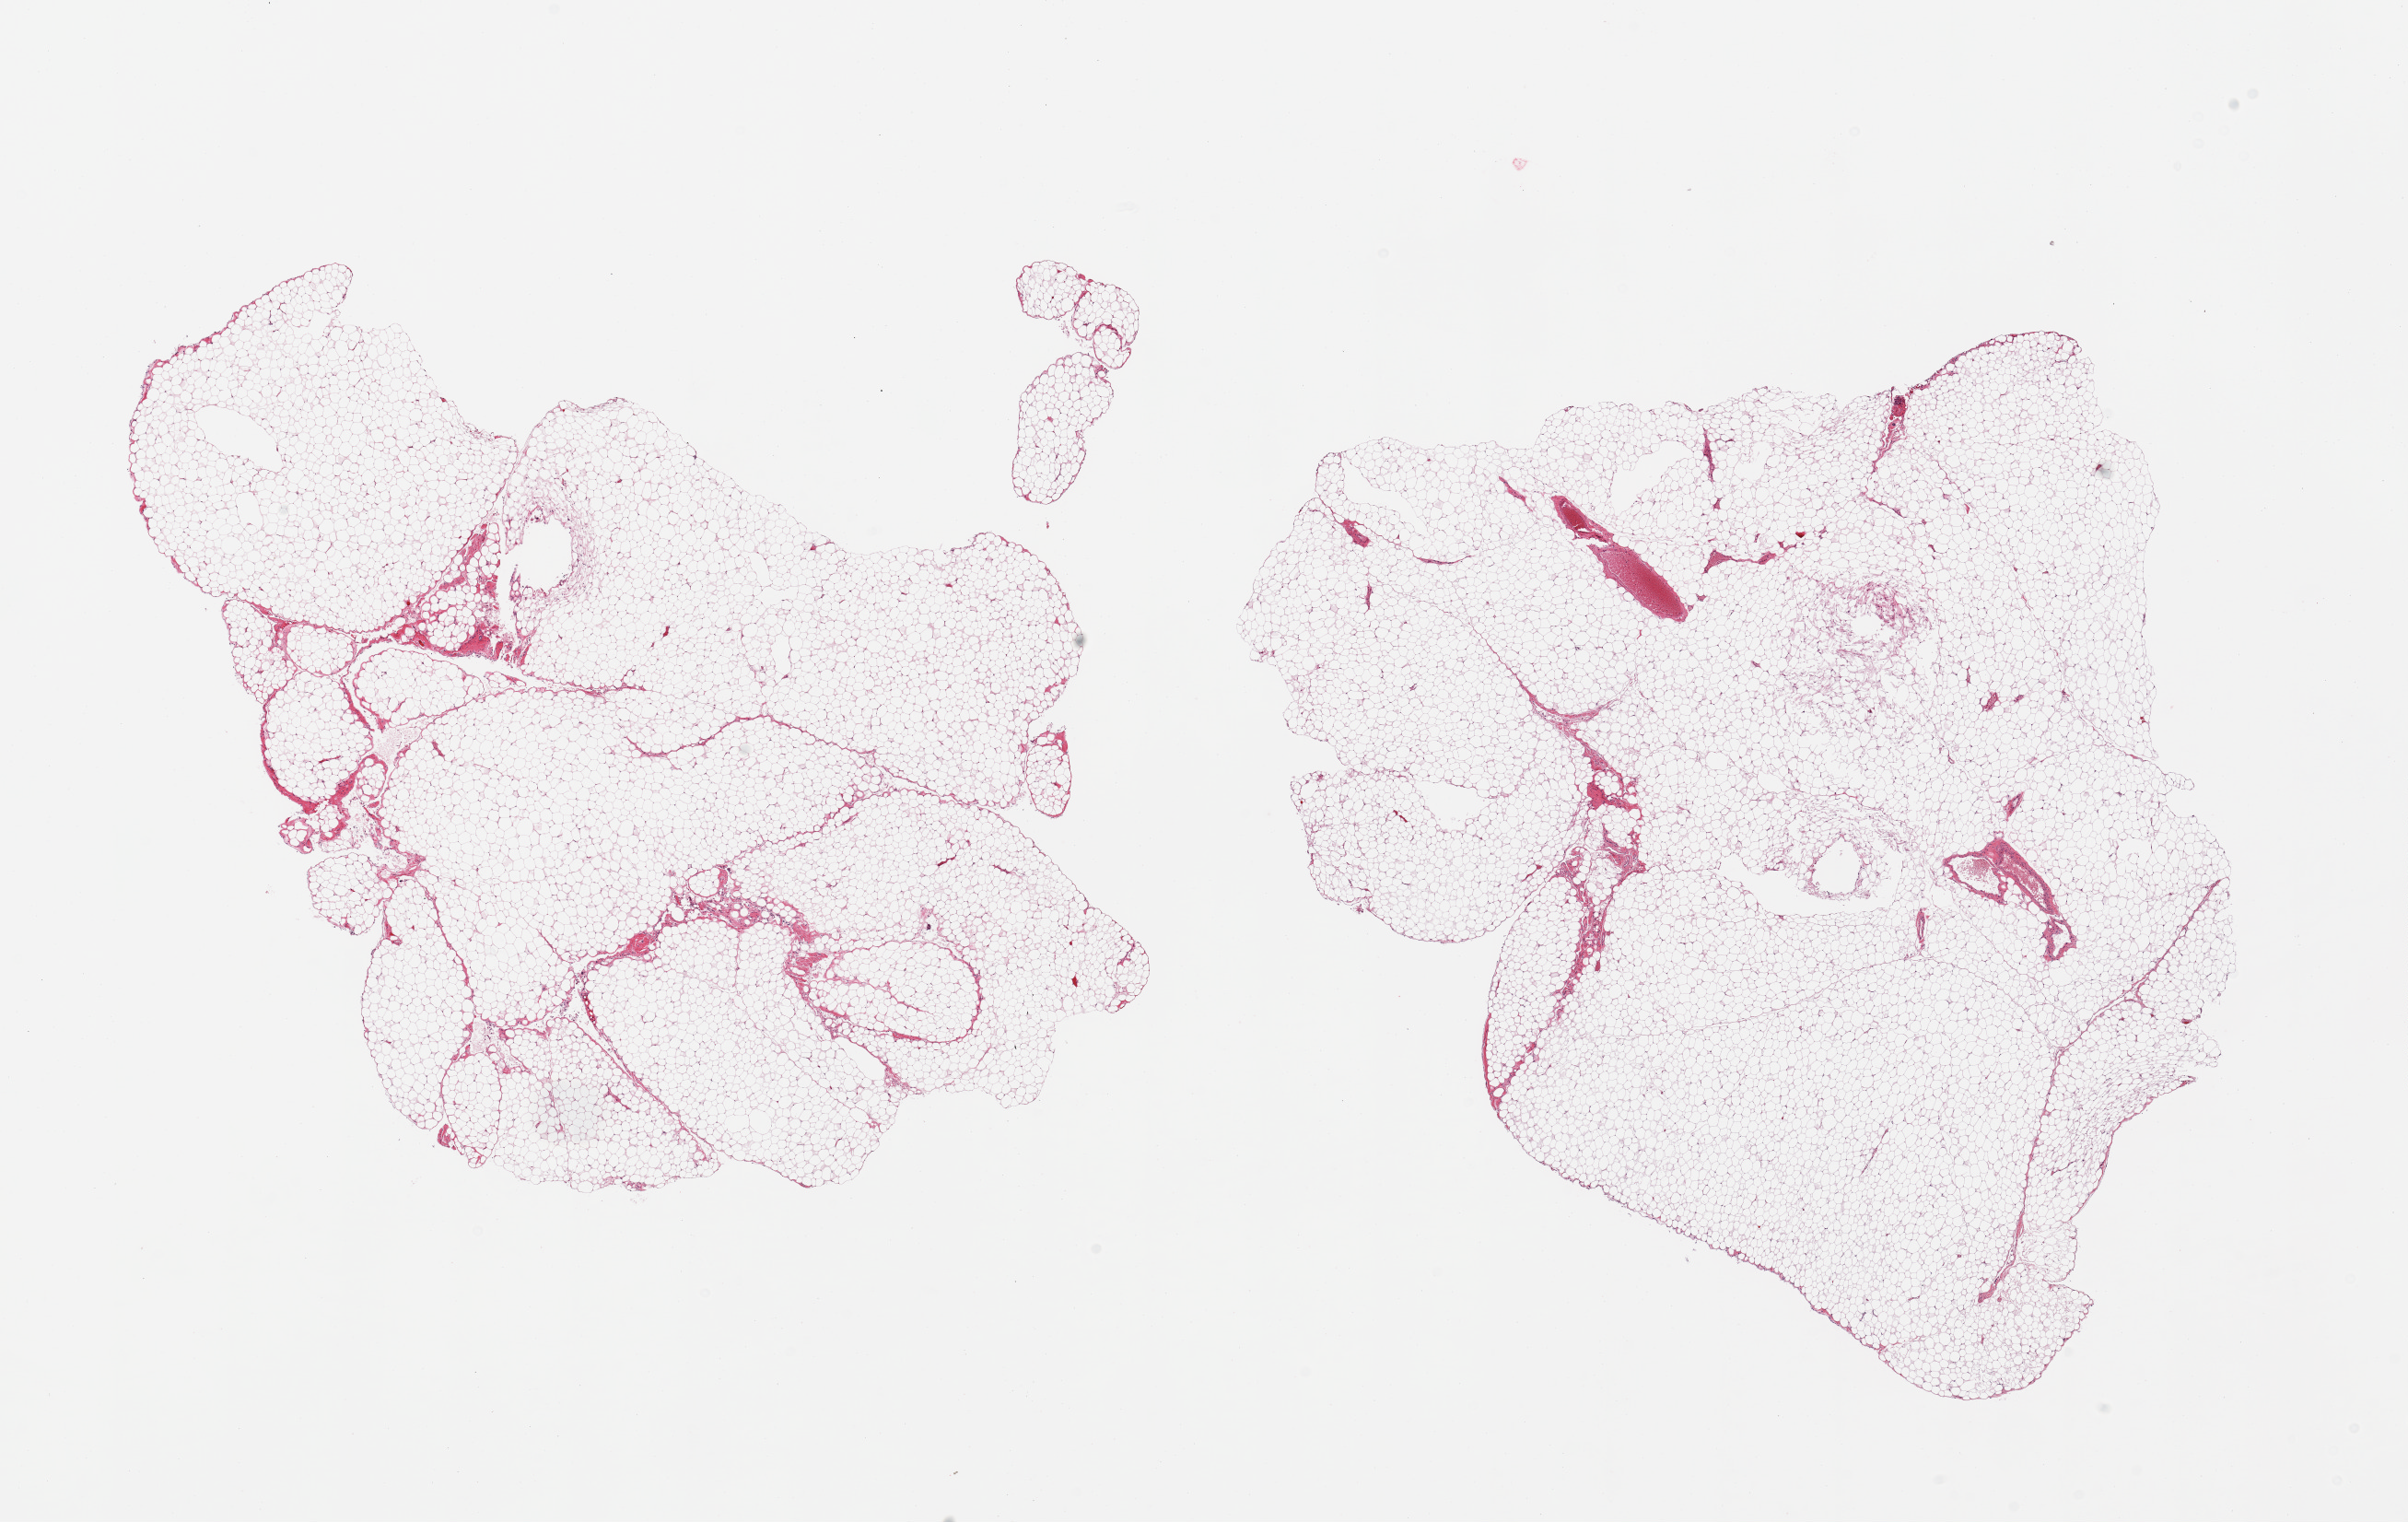
H&E whole-slide image, brightfield, whole scanned area (about 20.7 x 13.1 mm) shown as a low-resolution overview, PAXgene-fixed paraffin-embedded (PFPE) section, target tissue: omentum, donor tissue sample. Donor: female.
Pathologist's review note for this sample: 2 pieces; mature adipose tissue.